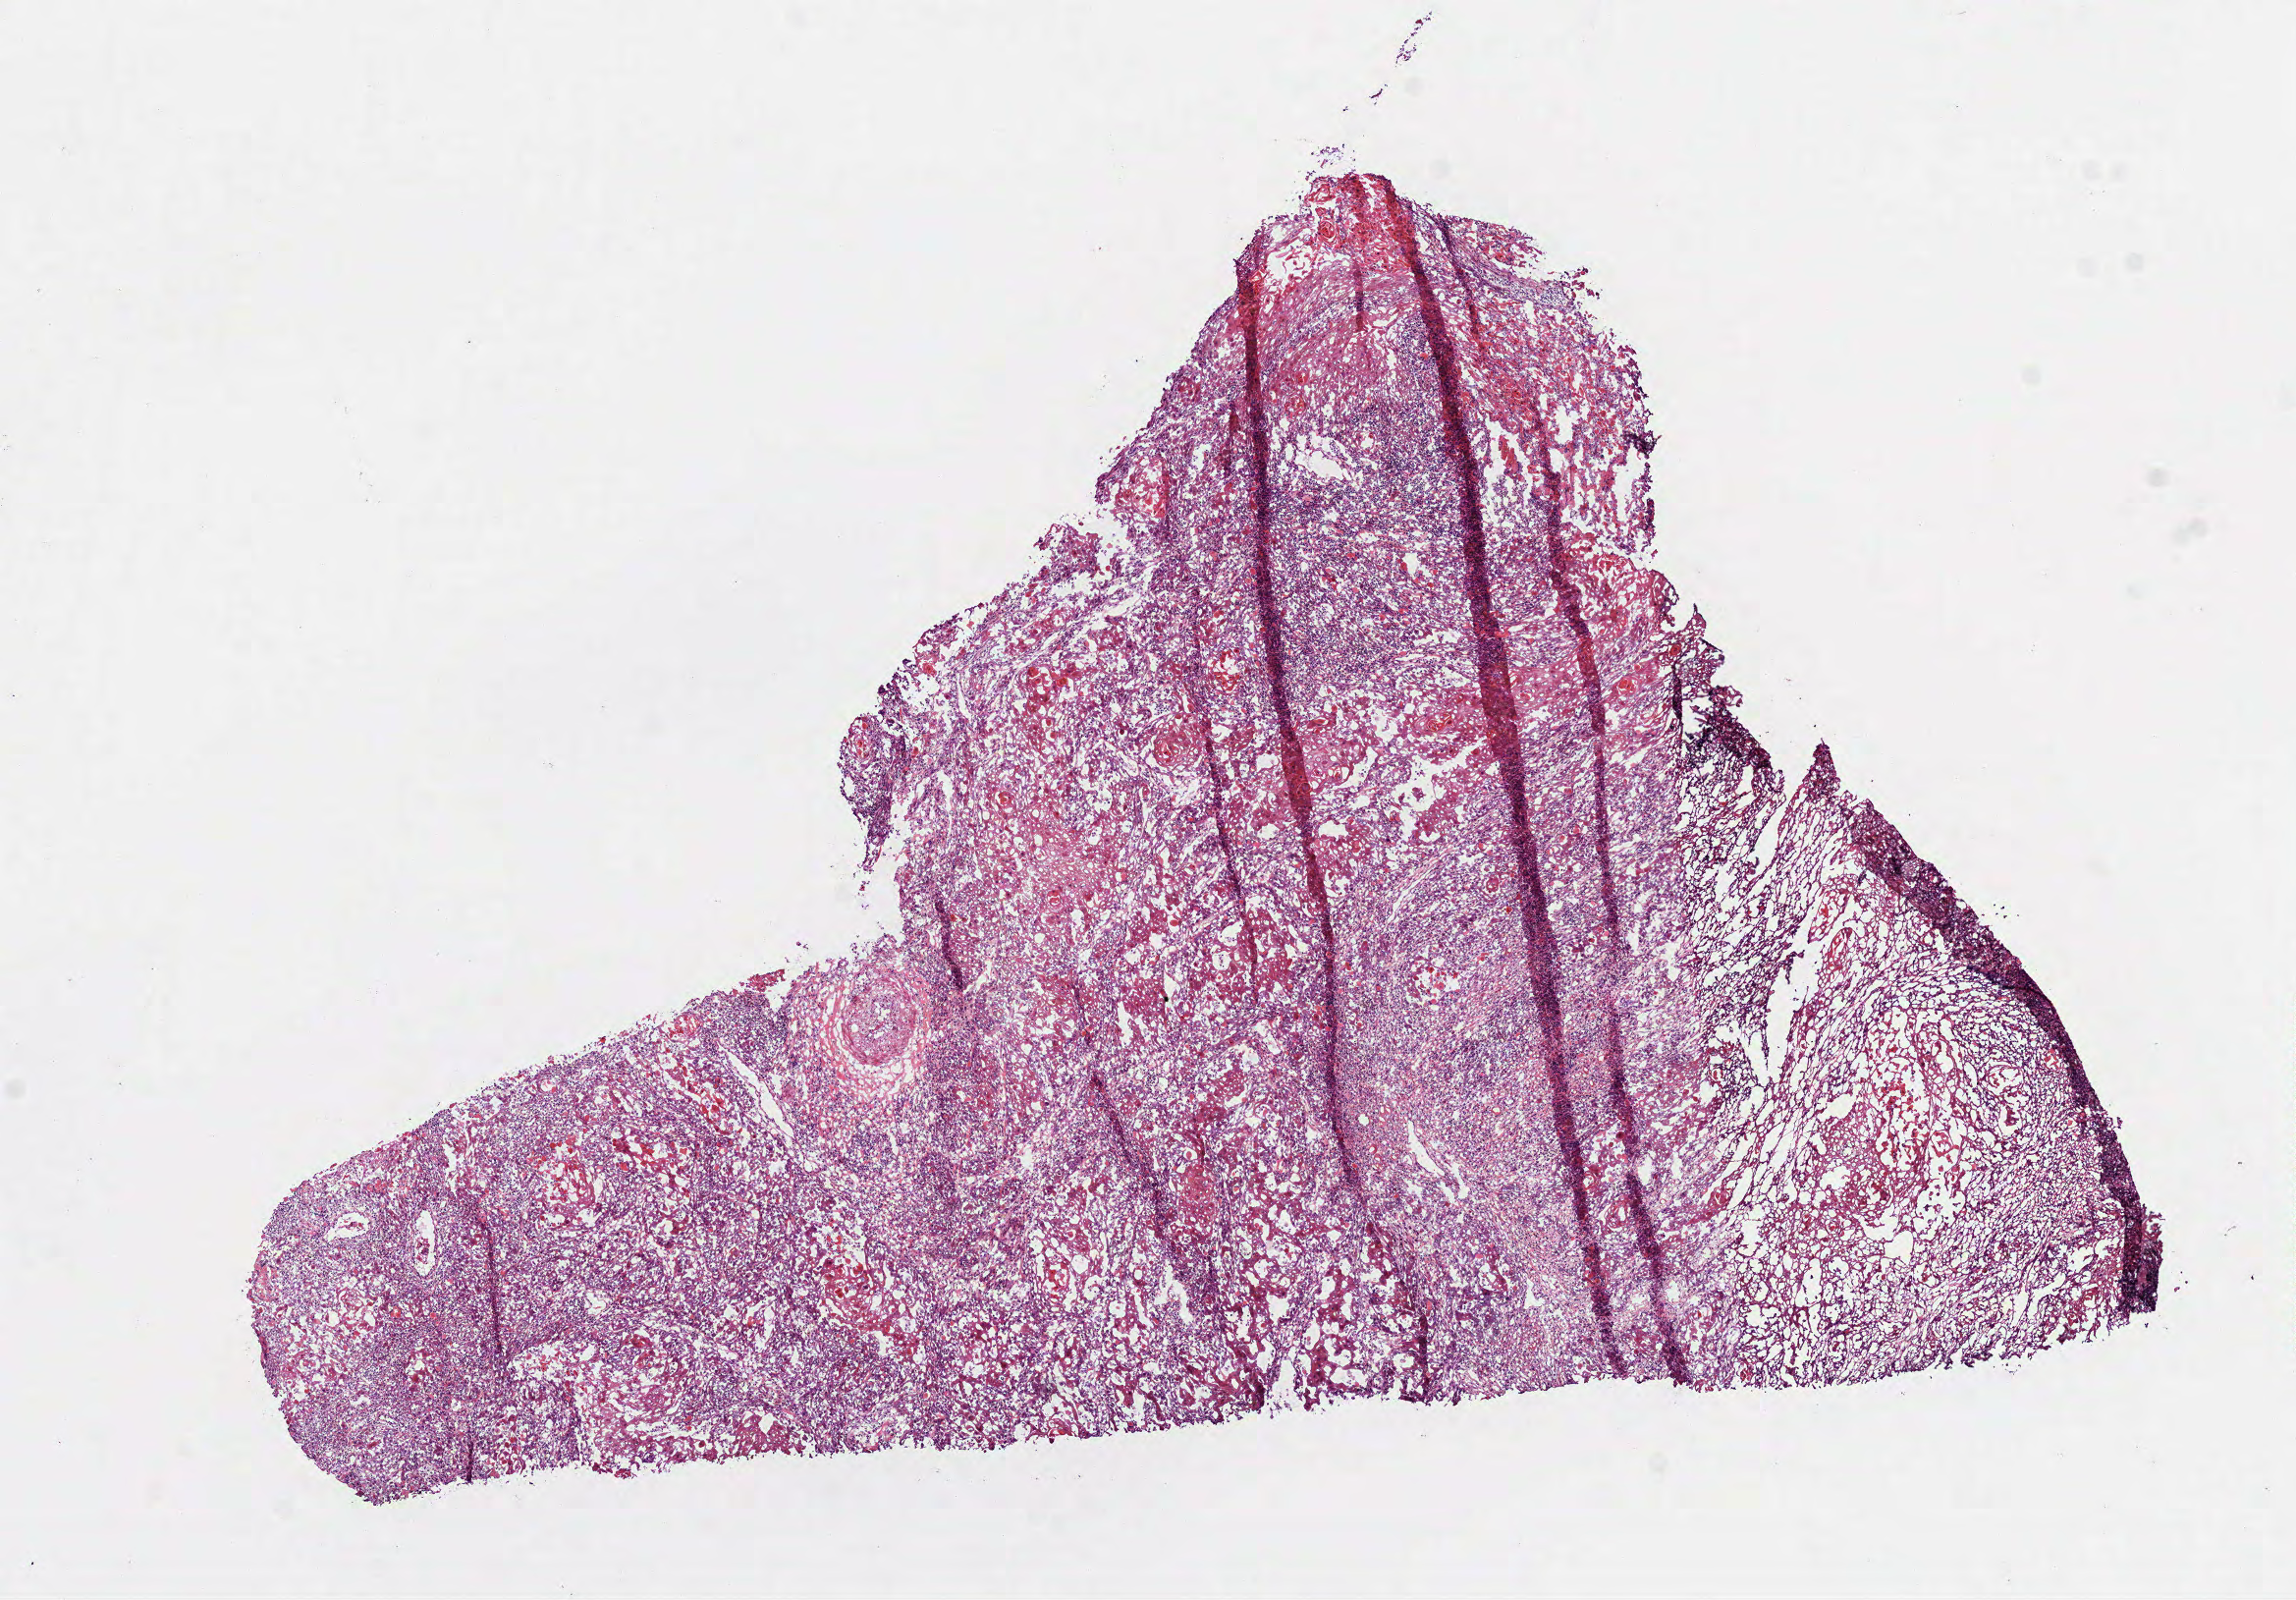
Whole-slide histology image, H&E, low-resolution overview of the scanned area, about 9.4 x 6.6 mm, frozen section from the bottom of the tissue portion, primary tumour sample from the head and neck. Female patient; age at initial diagnosis 83 years. Histologic grade: G2 (moderately differentiated). Composition of this section per pathologist review: tumour cells 90%, tumour nuclei 62%, normal cells 0%, stromal cells 10%, necrosis 0%. Inflammatory infiltration, as recorded: lymphocyte infiltration 30%.
* TNM: T3 N1 M0
* laterality: left
* AJCC pathologic stage: III (6th edition)
* diagnosis: Squamous cell carcinoma, NOS (mouth, NOS)